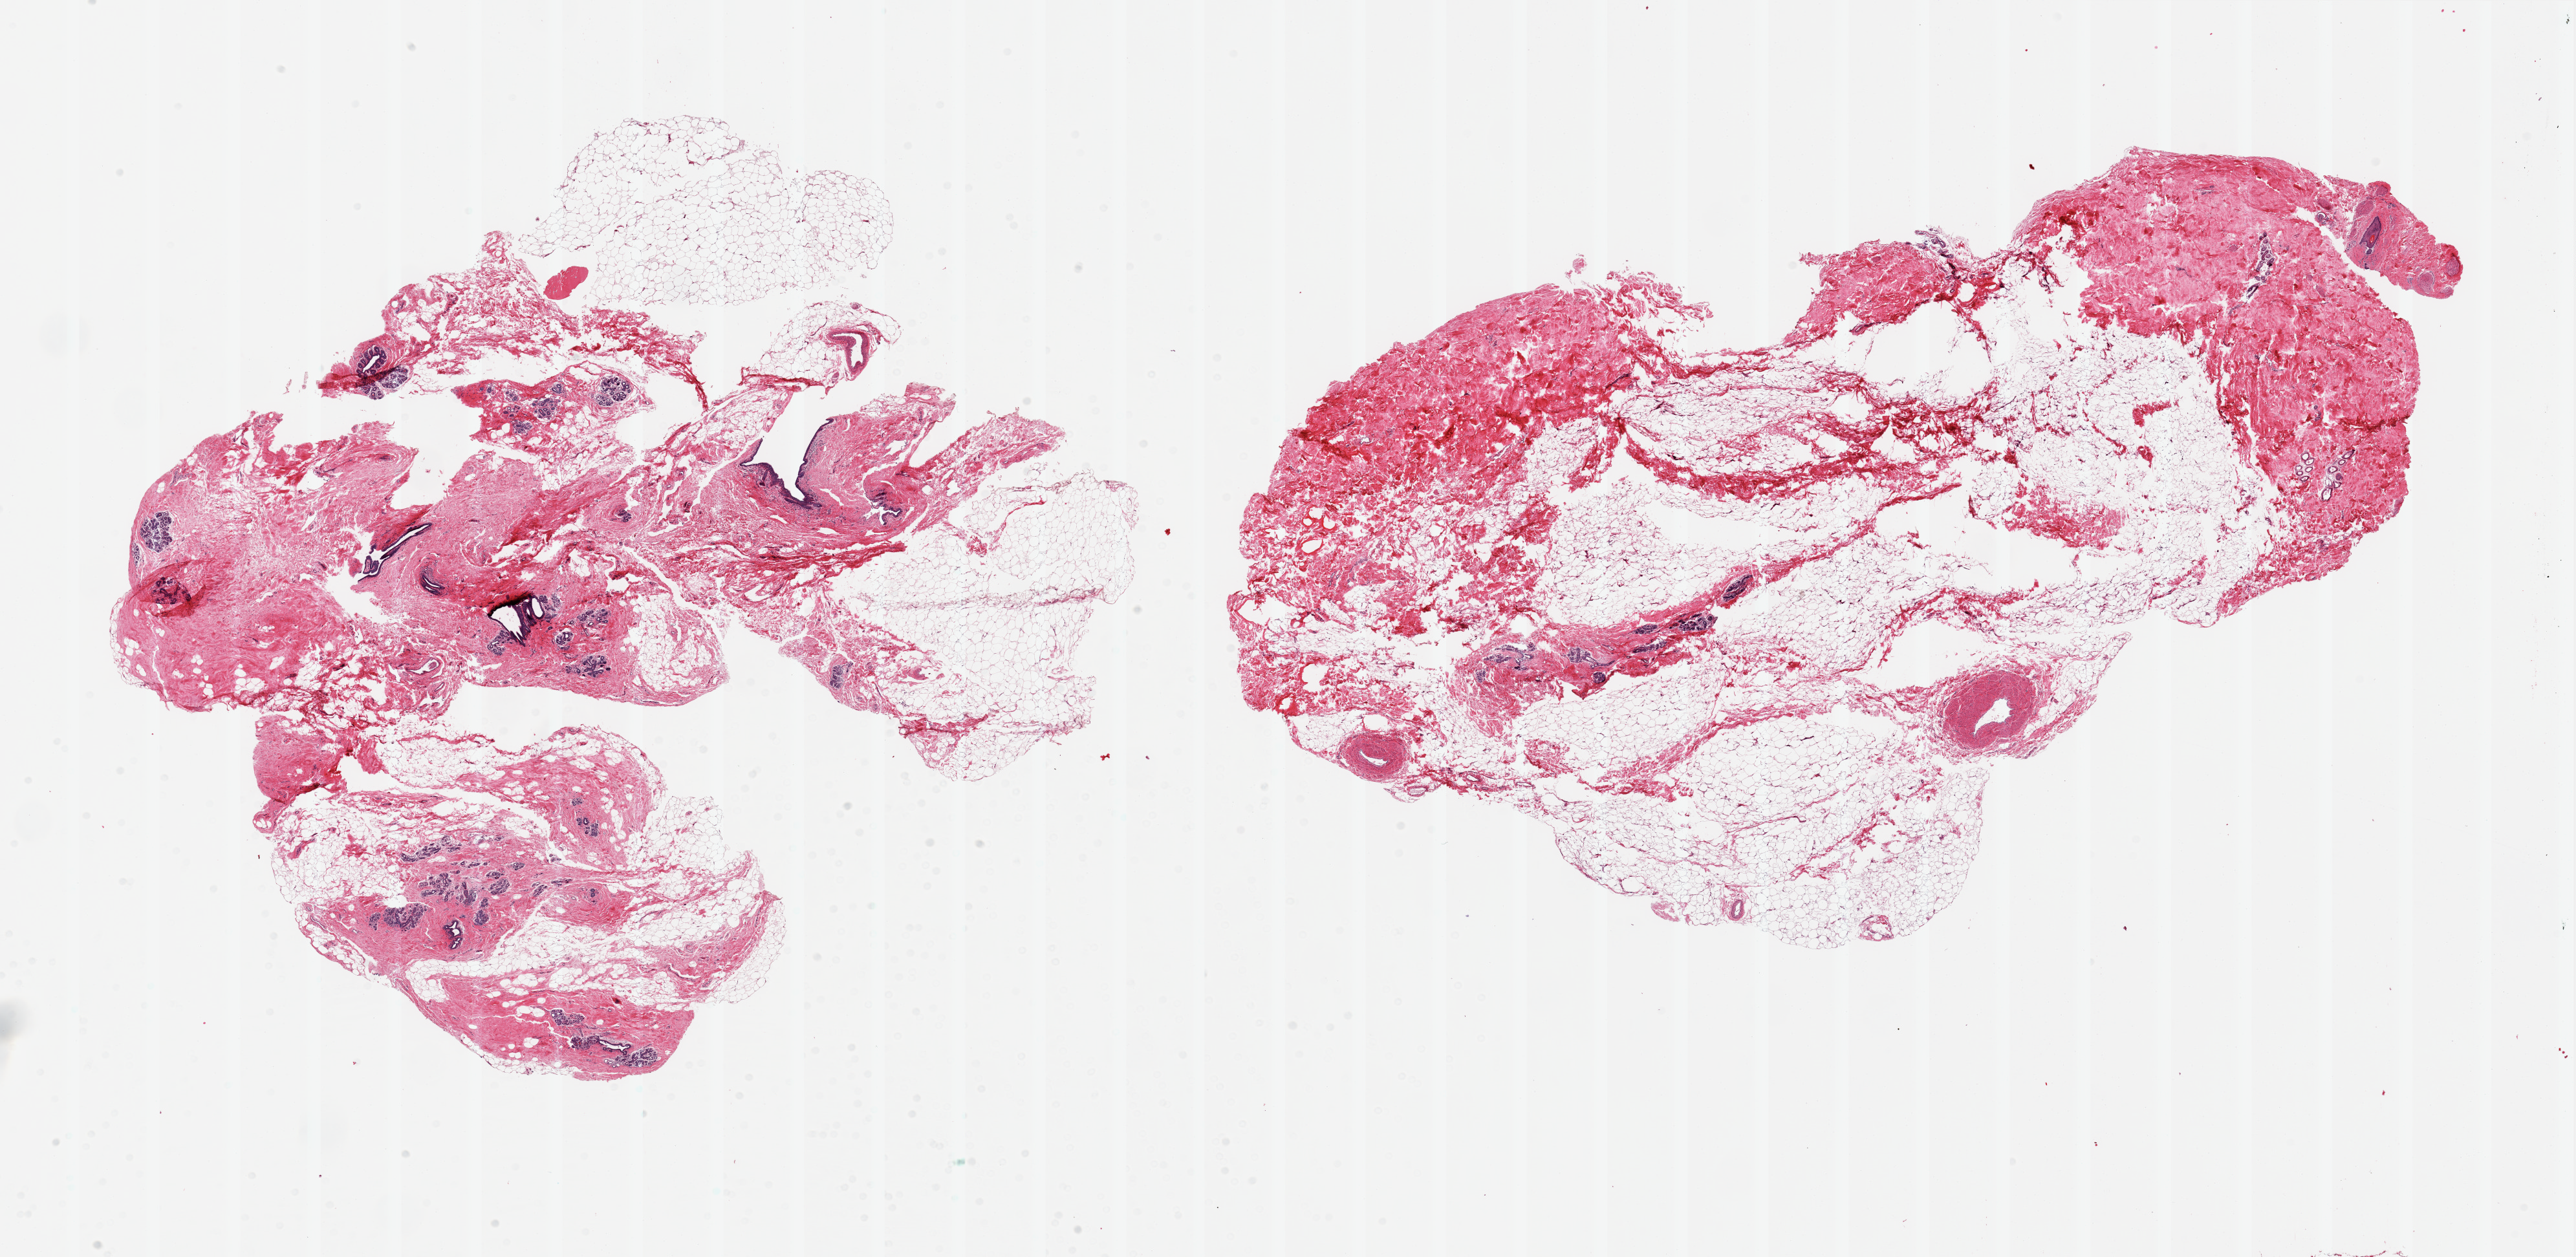
Hematoxylin and eosin (H&E) whole-slide image, low-resolution overview of the scanned area, about 31.5 x 15.4 mm. PAXgene-fixed, paraffin-embedded tissue. Section of breast (target tissue). Tissue donor sample.
Reviewer comment on this tissue sample: 2 pieces; ductal and lobular units present; 1 piece has 40% fat, other has 80% fat.